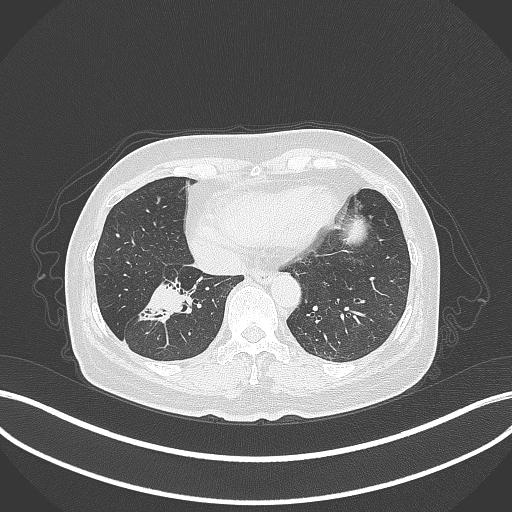
Chest CT, one axial slice; slice 118 of 429 in the series (ordered by position); reconstruction kernel B70f; lung window (W 1500 / L -600 HU); 1 mm slice thickness; 512 × 512 image matrix, field of view 400 × 400 mm. Female patient, age 67 years. Case-level facts recorded for this patient, not image findings: clinical TNM (as recorded): T1c N1 M0.
Structures marked on this image (bounding box drawn by a radiologist):
- lung tumour (recorded histology: adenocarcinoma): bounding box <134,278,194,333> (left, top, right, bottom; pixels)